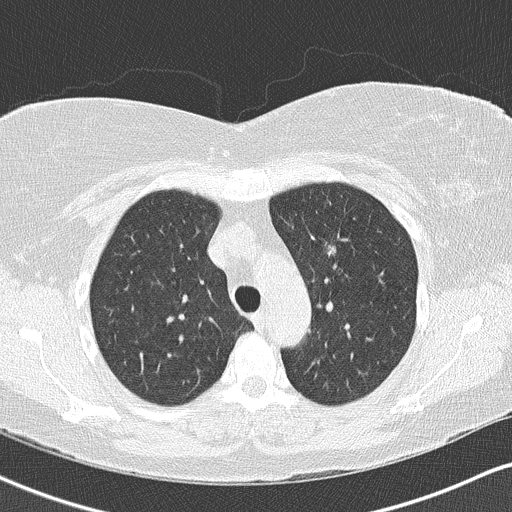
Low-dose screening chest CT, axial slice, second annual screen, lung window (W 1500 / L -600 HU), lung (sharp) reconstruction kernel (B50f), 512 × 512 image matrix, field of view 328 × 328 mm. Female participant, aged 57 years at enrolment. Current smoker at enrolment.
• Lesion marked by an expert reader, bounding box [x1, y1, x2, y2] px = [313, 225, 348, 267].
• The screening reader recorded 3 non-calcified nodules or masses ≥4 mm on this exam (left upper lobe, right upper lobe, right middle lobe); which of them this box marks is not recorded.
• Official screen result: positive, other.